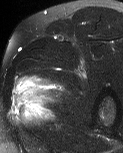
MRI of an extremity soft-tissue mass, one axial slice; position 44 of 60 along the scan axis; T2-weighted fat-saturated; MR volume resampled by the dataset authors to the PET/CT grid (not the native acquisition matrix); 3.27 mm slice thickness; 123 × 153 image matrix. Male patient. From the clinical record (not read from this slice): histological type: pleiomorphic liposarcoma; grade: high; site of the primary tumour: left thigh.
Outlined on this slice (expert contour drawn on MRI and transferred to this co-registered scan by the dataset authors):
- gross tumour volume including surrounding oedema: bounding box (x1, y1, x2, y2) in pixels: (11, 77, 66, 128)